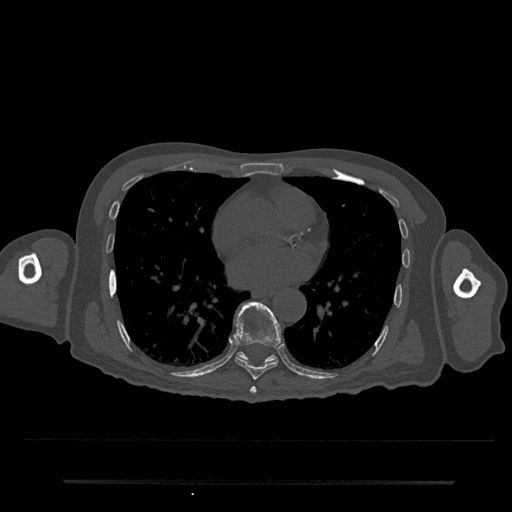
CT including the spine, one axial slice. Slice 407 of 797 in the series (ordered by position). 120 kVp. Bone window (W 1800 / L 400 HU). 0.5 mm slice thickness. 512 × 512 image matrix, field of view 427 × 427 mm. Patient: male, 74 years. Case-level facts recorded for this patient, not image findings: primary cancer: prostate.
Annotated regions visible in this slice (semi-automatically segmented with operator editing):
- T7 vertebra: bounding box [x1, y1, x2, y2] px = [250, 386, 256, 394]
- T8 vertebra: [234, 301, 282, 380]
- T9 vertebra: [238, 352, 277, 362]